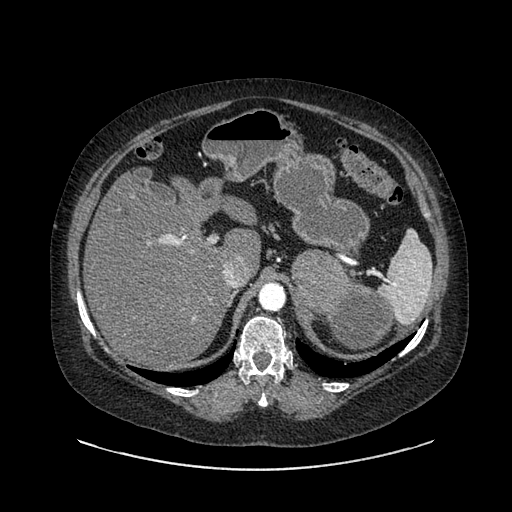
Contrast-enhanced abdominal CT, one axial slice; position 610 of 769 along the scan axis; reconstruction kernel SOFT; 120 kVp; intravenous contrast given; soft-tissue window (W 400 / L 40 HU); 0.62 mm slice thickness; 512 × 512 image matrix. Patient: female, 61 years. Case-level facts recorded for this patient, not image findings: diagnosis: adrenocortical carcinoma; tumour side: left adrenal; tumour size at pathology: 13 cm; Ki-67 index: 79 %; stage (as recorded): 2.
Outlined on this slice (semi-automatic segmentation, software-assisted and operator-edited):
- mass: bounding box [x1, y1, x2, y2] px = [293, 252, 392, 349]